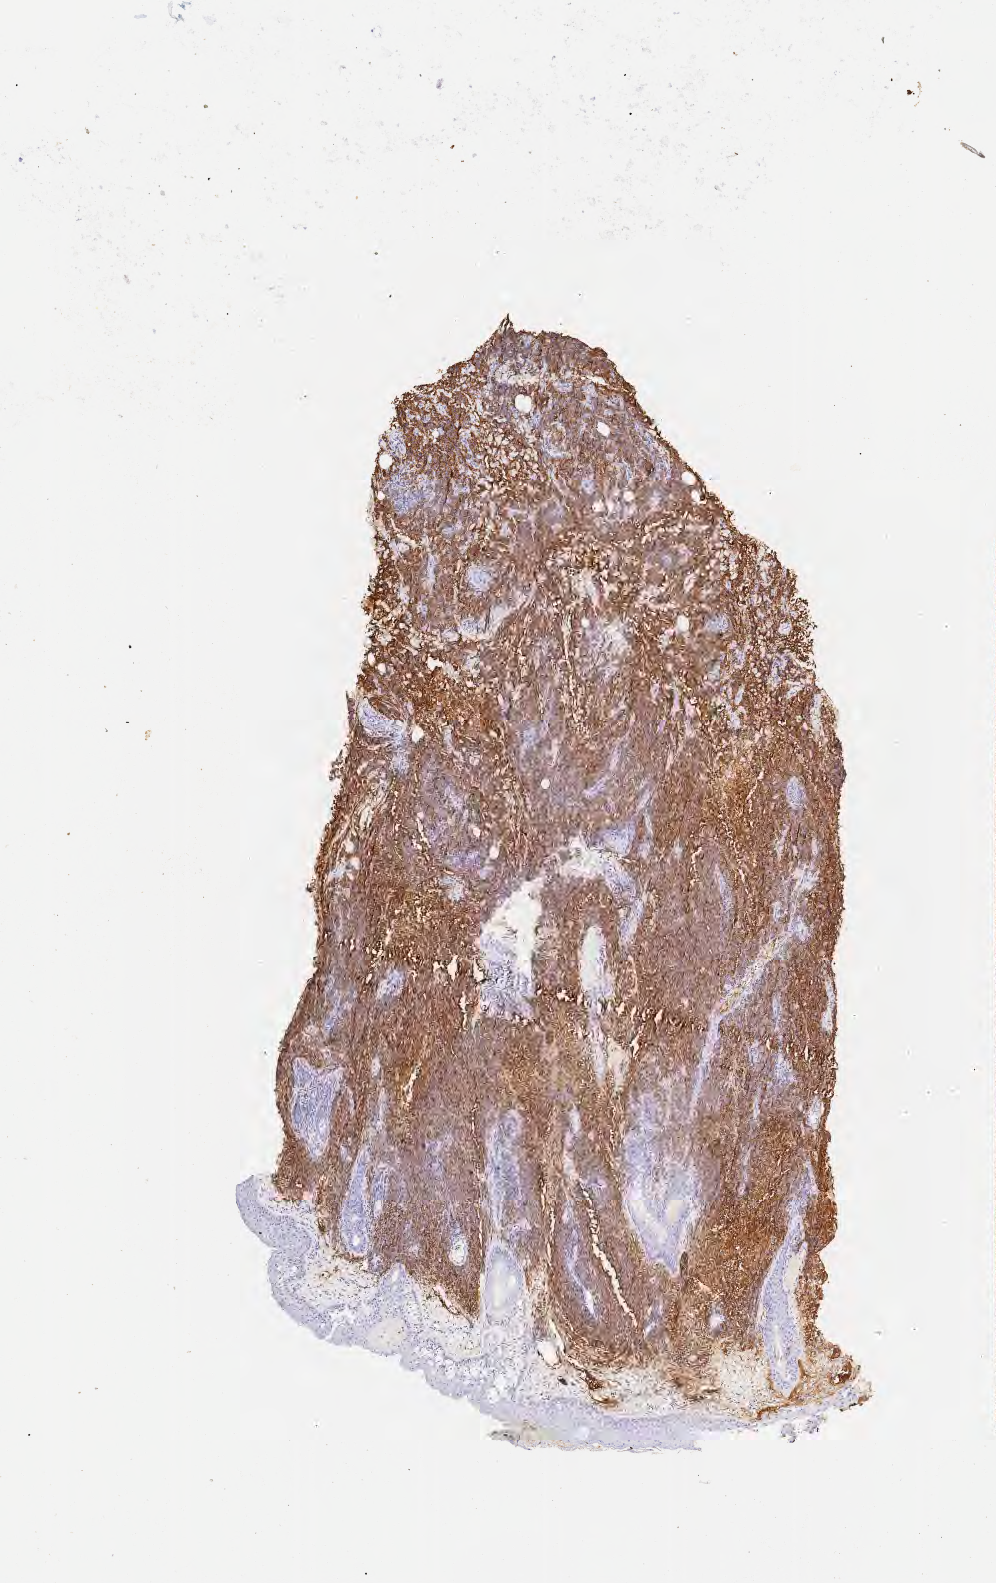
Immunohistochemistry (IHC) whole-slide image stained for CD20 — shown as a low-resolution overview of the whole scanned area (about 4.0 x 6.4 mm). Specimen: tumor tissue. Patient: male, aged 41.
* diagnosis: Diffuse large B-cell lymphoma, NOS